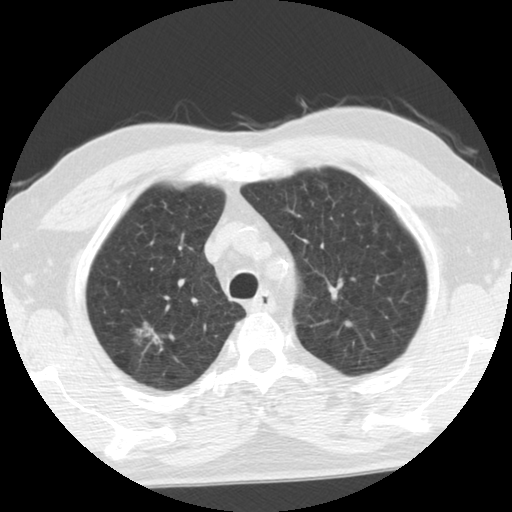
Low-dose screening chest CT, one axial slice; position 90 of 116 along the scan axis; 140 kVp; lung window (W 1500 / L -600 HU); 512 × 512 image matrix.
Structures marked on this image (manually delineated by an expert):
- lesion 1 (tumor, upper lobe of right lung): bounding box (x1, y1, x2, y2) in pixels: (130, 321, 164, 353)